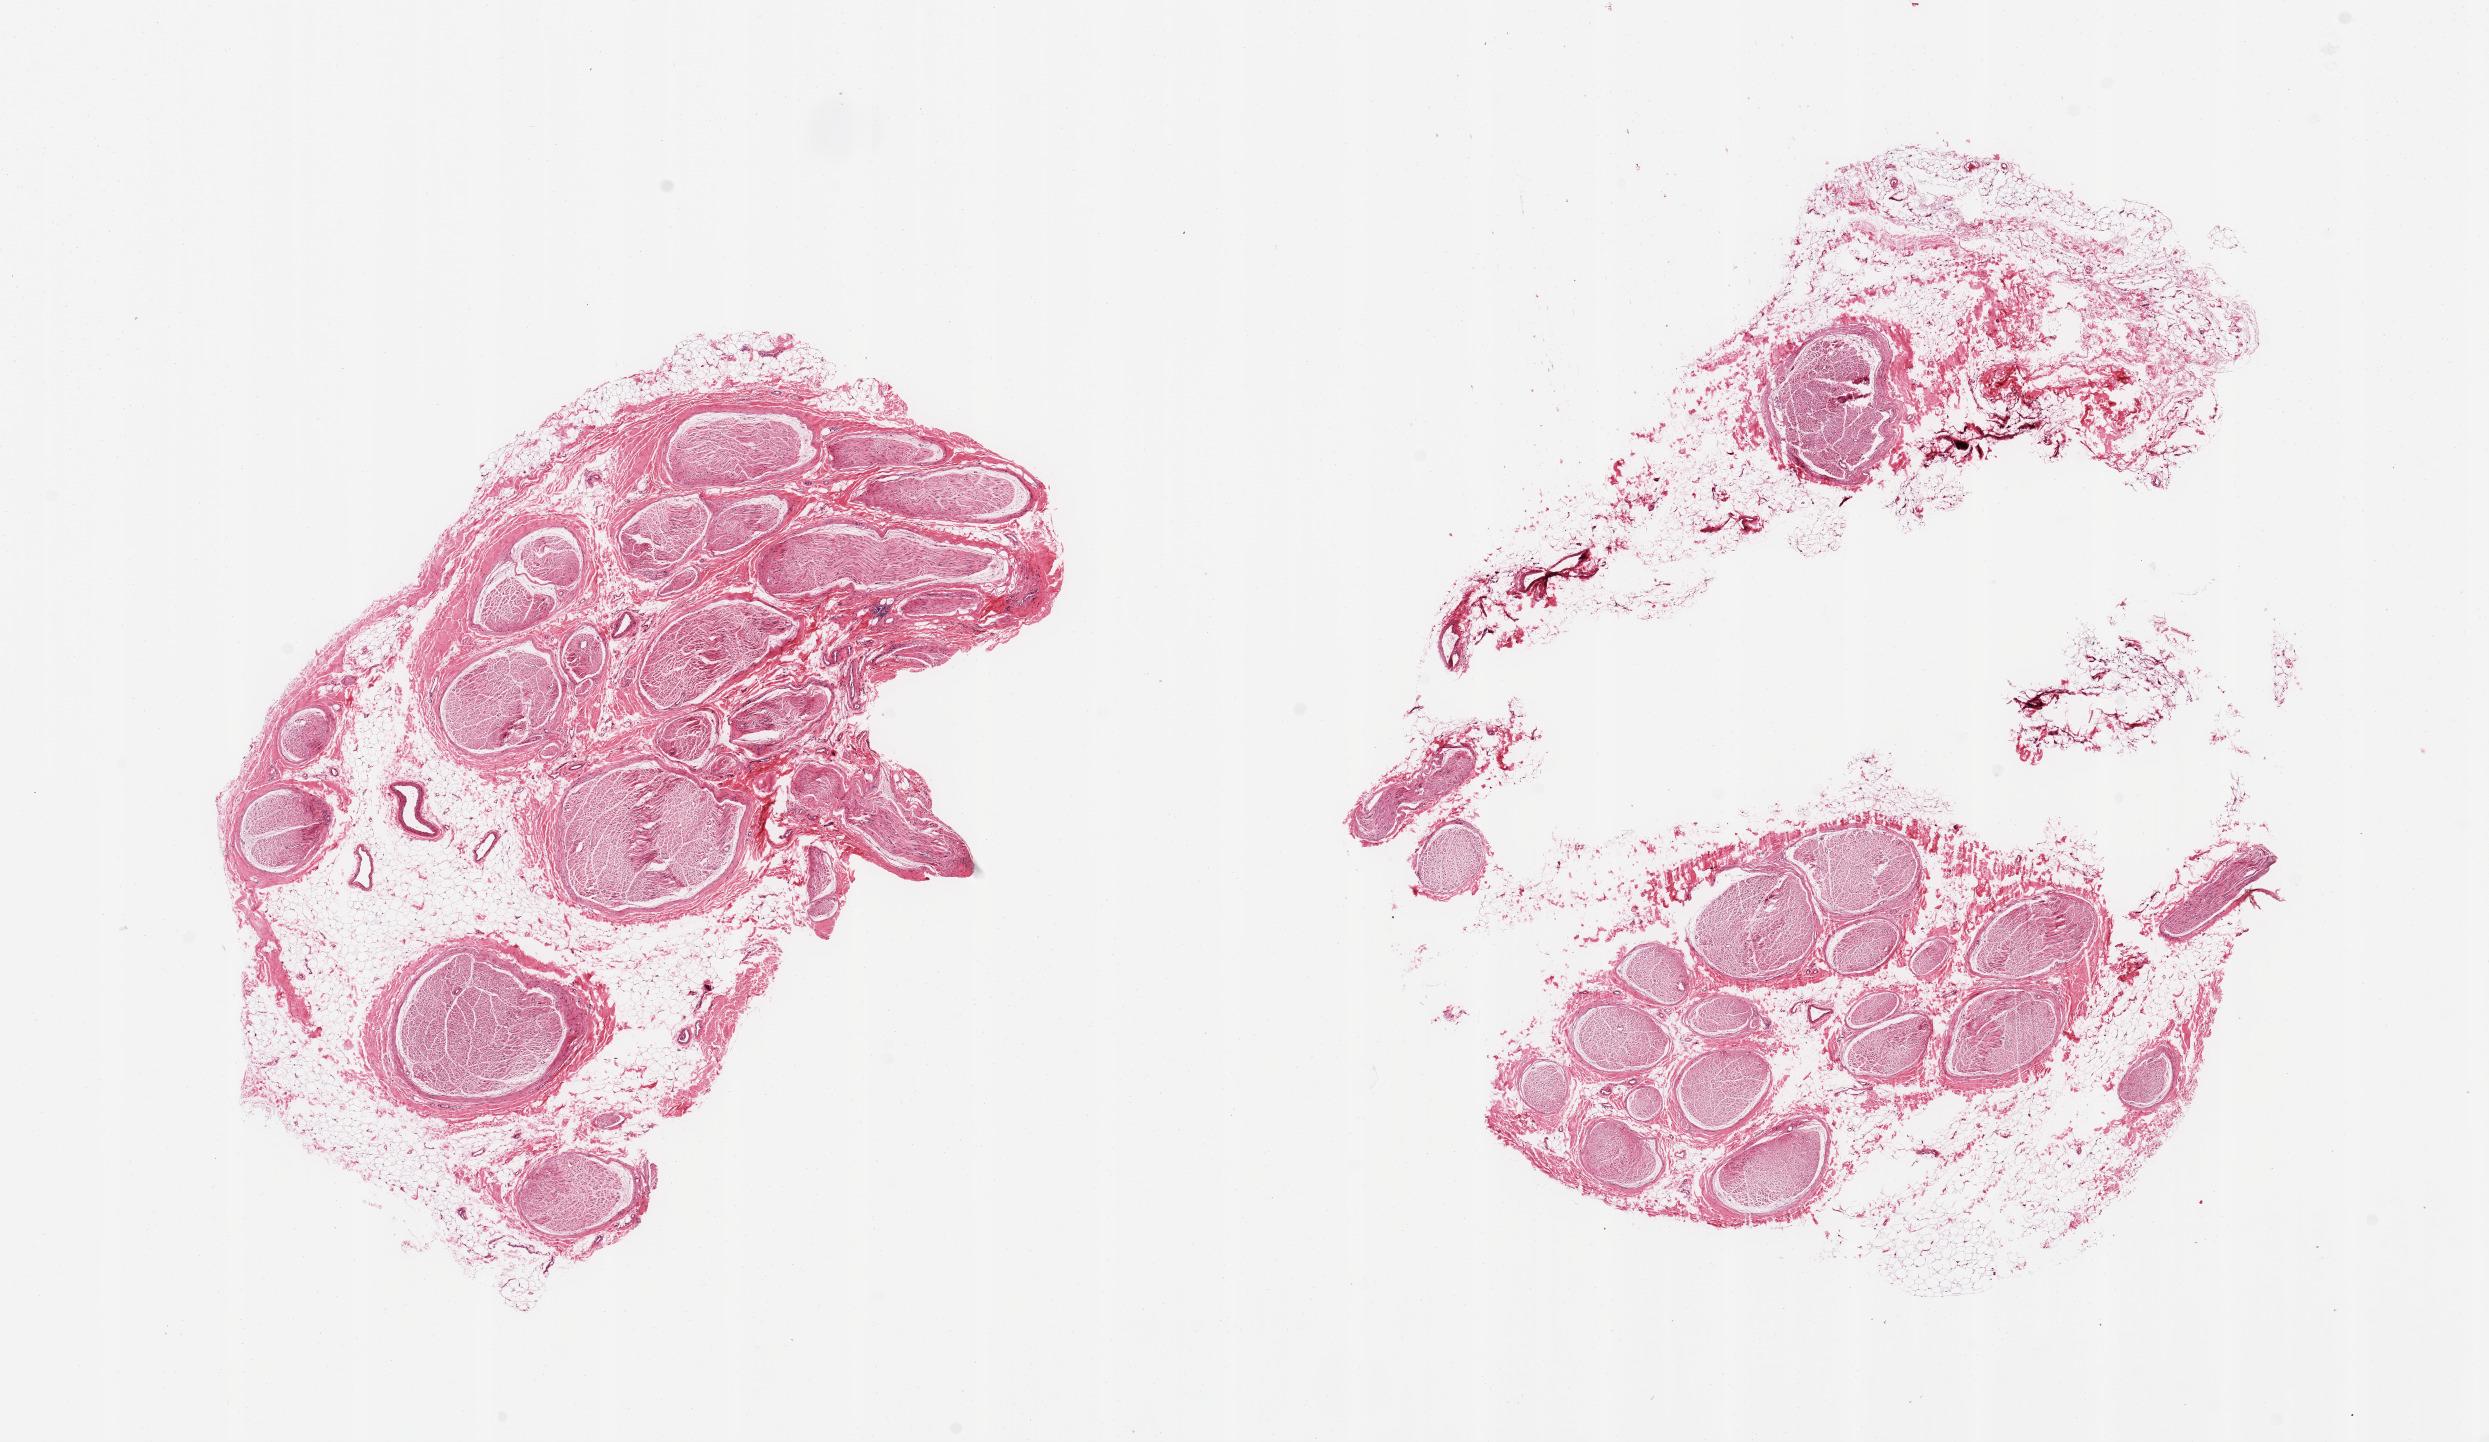
Hematoxylin and eosin (H&E) whole-slide image — low-resolution overview of the scanned area, about 19.7 x 11.4 mm (slide scanned at 20x), PAXgene-fixed, paraffin-embedded tissue, target tissue: tibial nerve, tissue donor sample. Donor: male.
• reviewer comment on this tissue sample: 2 pieces, partial rim of adherent fat up to ~2mm